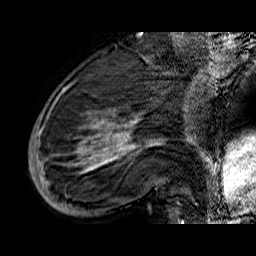
Breast MRI (dynamic contrast-enhanced), one sagittal slice. Slice 19 of 60 in the series (ordered by position). Dynamic contrast-enhanced series, time point 2 of 6 at this slice position (early post-contrast). 1.5 T. TE 6.5 ms, TR 32.9 ms. 4 mm slice thickness. 256 × 256 image matrix. Female patient. From the clinical record (not read from this slice): setting: breast cancer imaged before/during neoadjuvant chemotherapy; receptor status: HR-positive, HER2-negative.
Annotated regions visible in this slice (semi-automatically segmented with operator editing):
- analysis volume of interest (the breast-tissue region the enhancement analysis was run in; not a lesion): bounding box (x1, y1, x2, y2) in pixels: (33, 74, 176, 210)
- tumour enhancement mask (voxels above the 100 % enhancement threshold inside the analysis volume of interest): (33, 100, 162, 209)